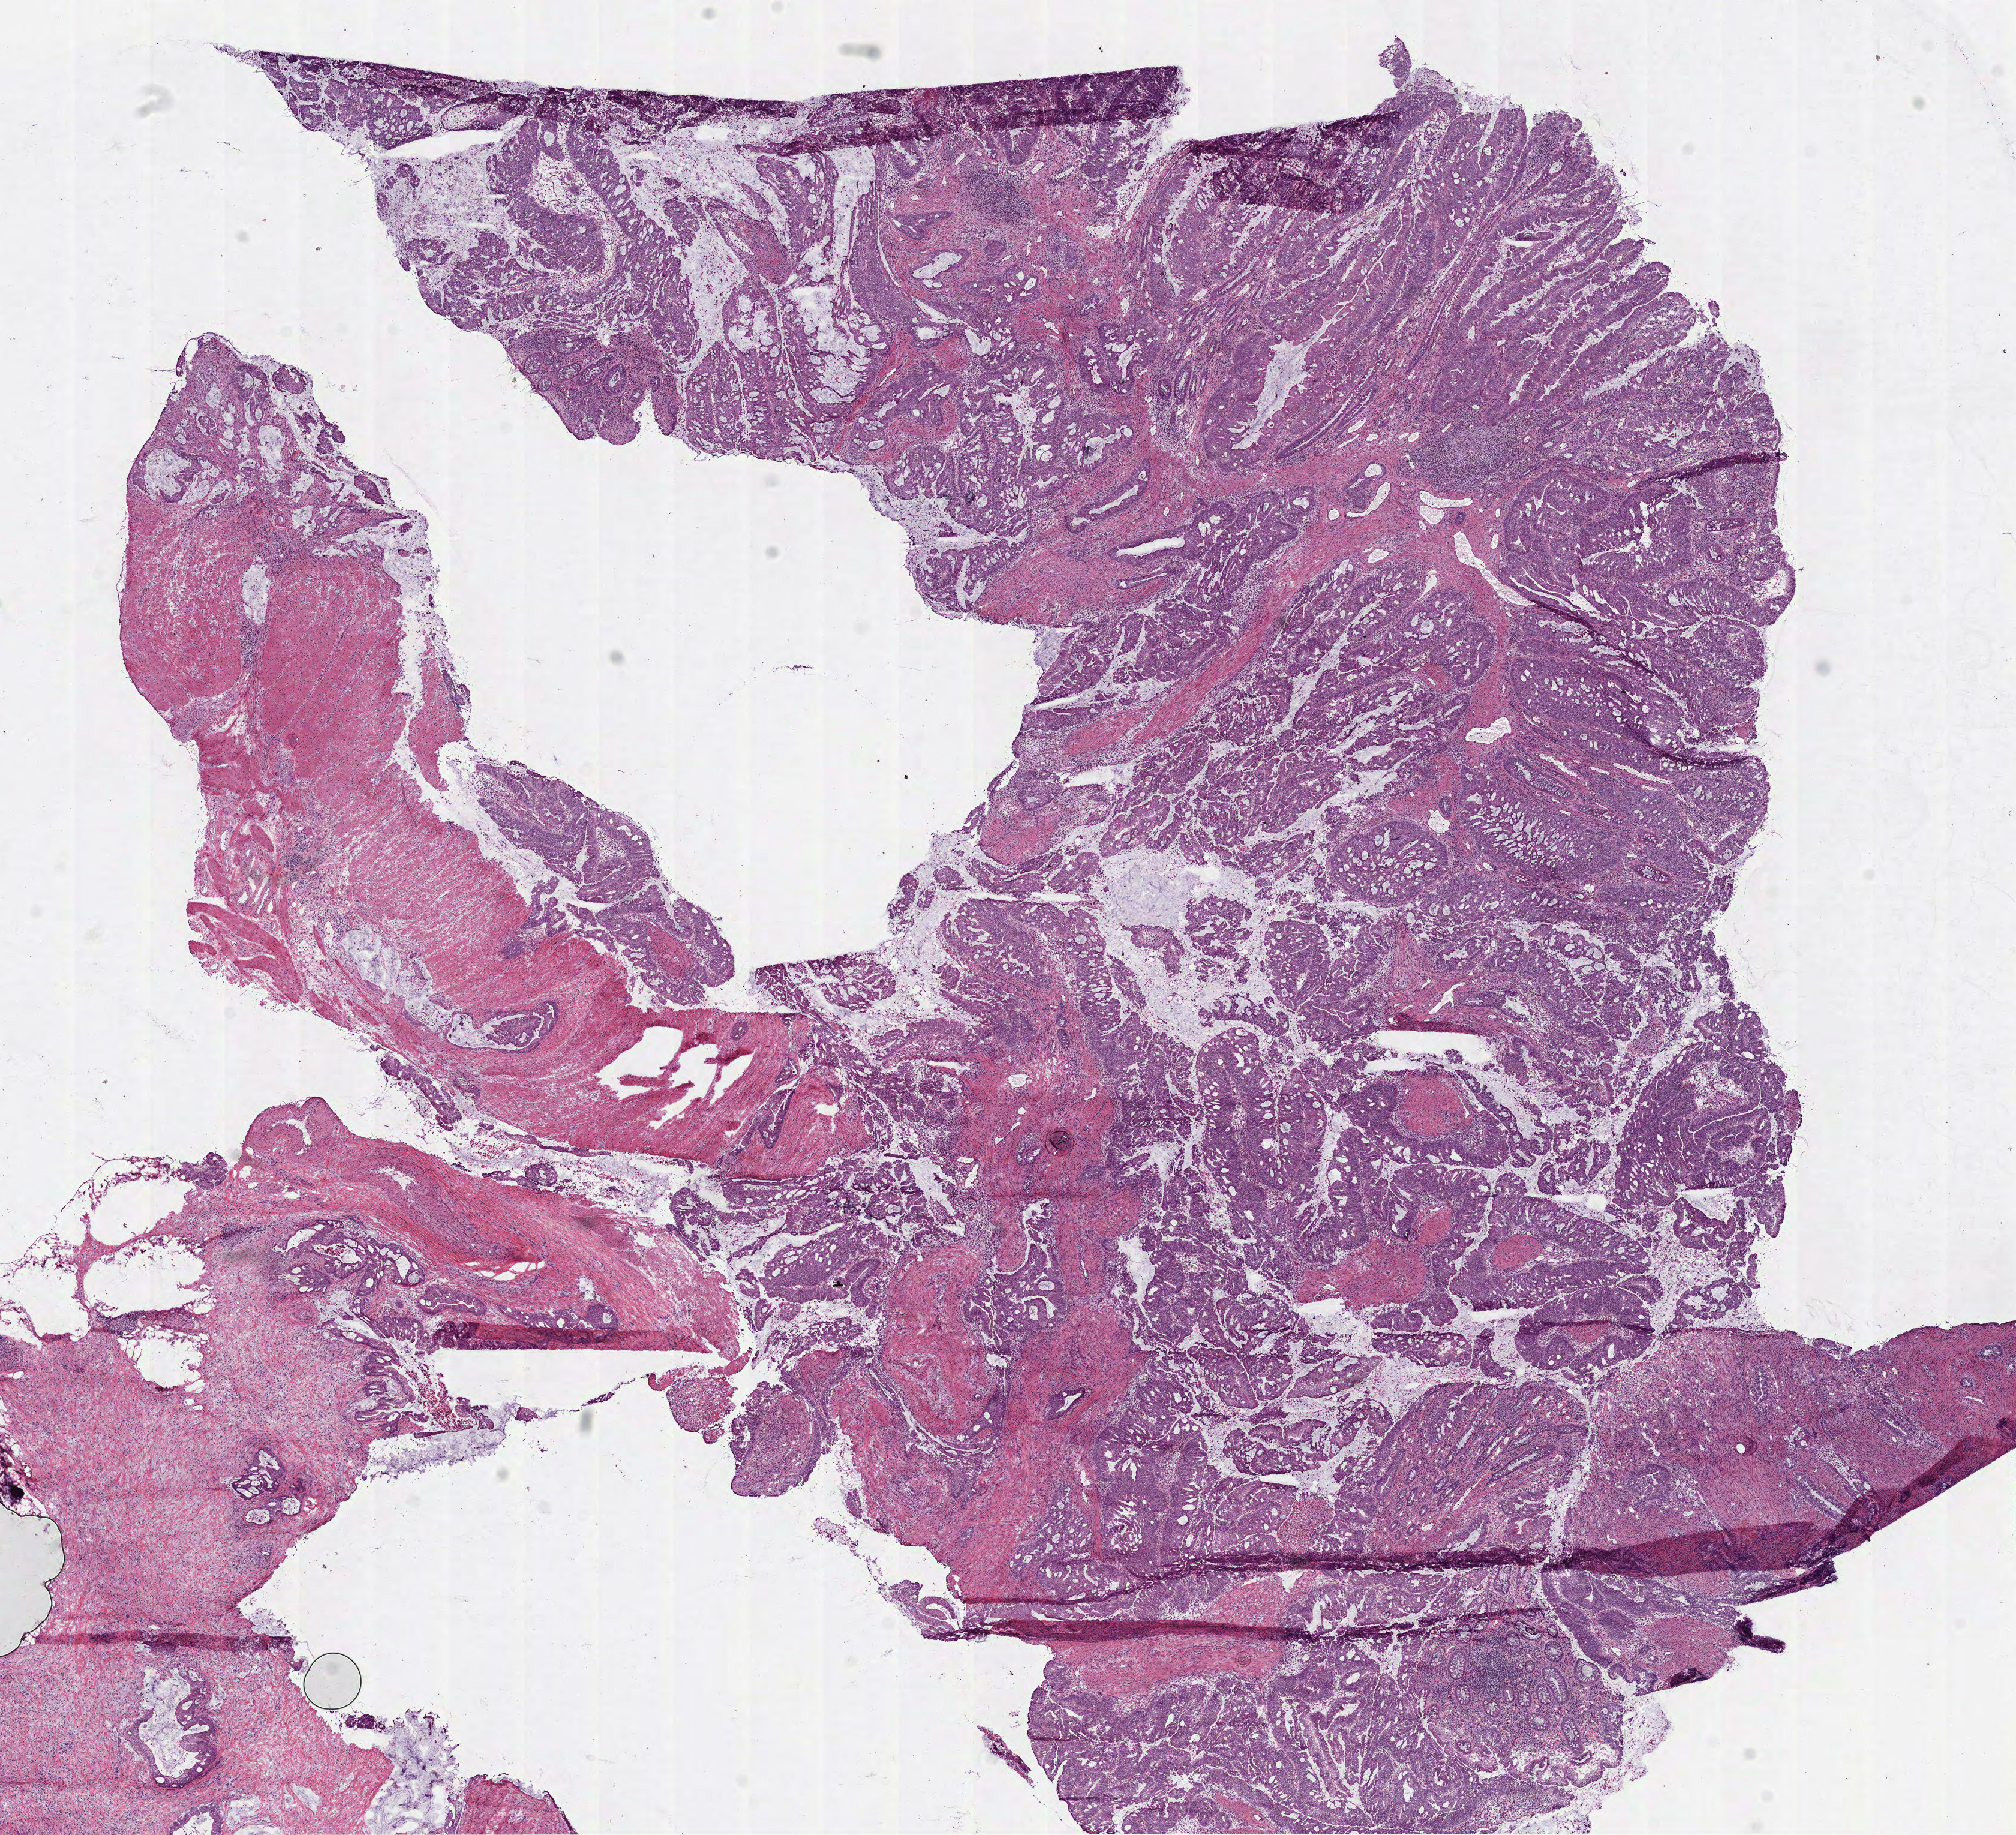
Hematoxylin and eosin (H&E) stained whole-slide image — shown as a low-resolution overview of the whole scanned area (about 13.6 x 12.3 mm, slide scanned at 40x). Frozen section from the bottom of the tissue portion. Sample: primary tumour, rectum. Female, age 70 years at initial diagnosis. Slide review estimates, as recorded: tumour cells 80%, tumour nuclei 80%, normal cells 0%, stromal cells 20%, necrosis 0%.
- AJCC pathologic stage: IVA (7th edition)
- diagnosis: Adenocarcinoma, NOS